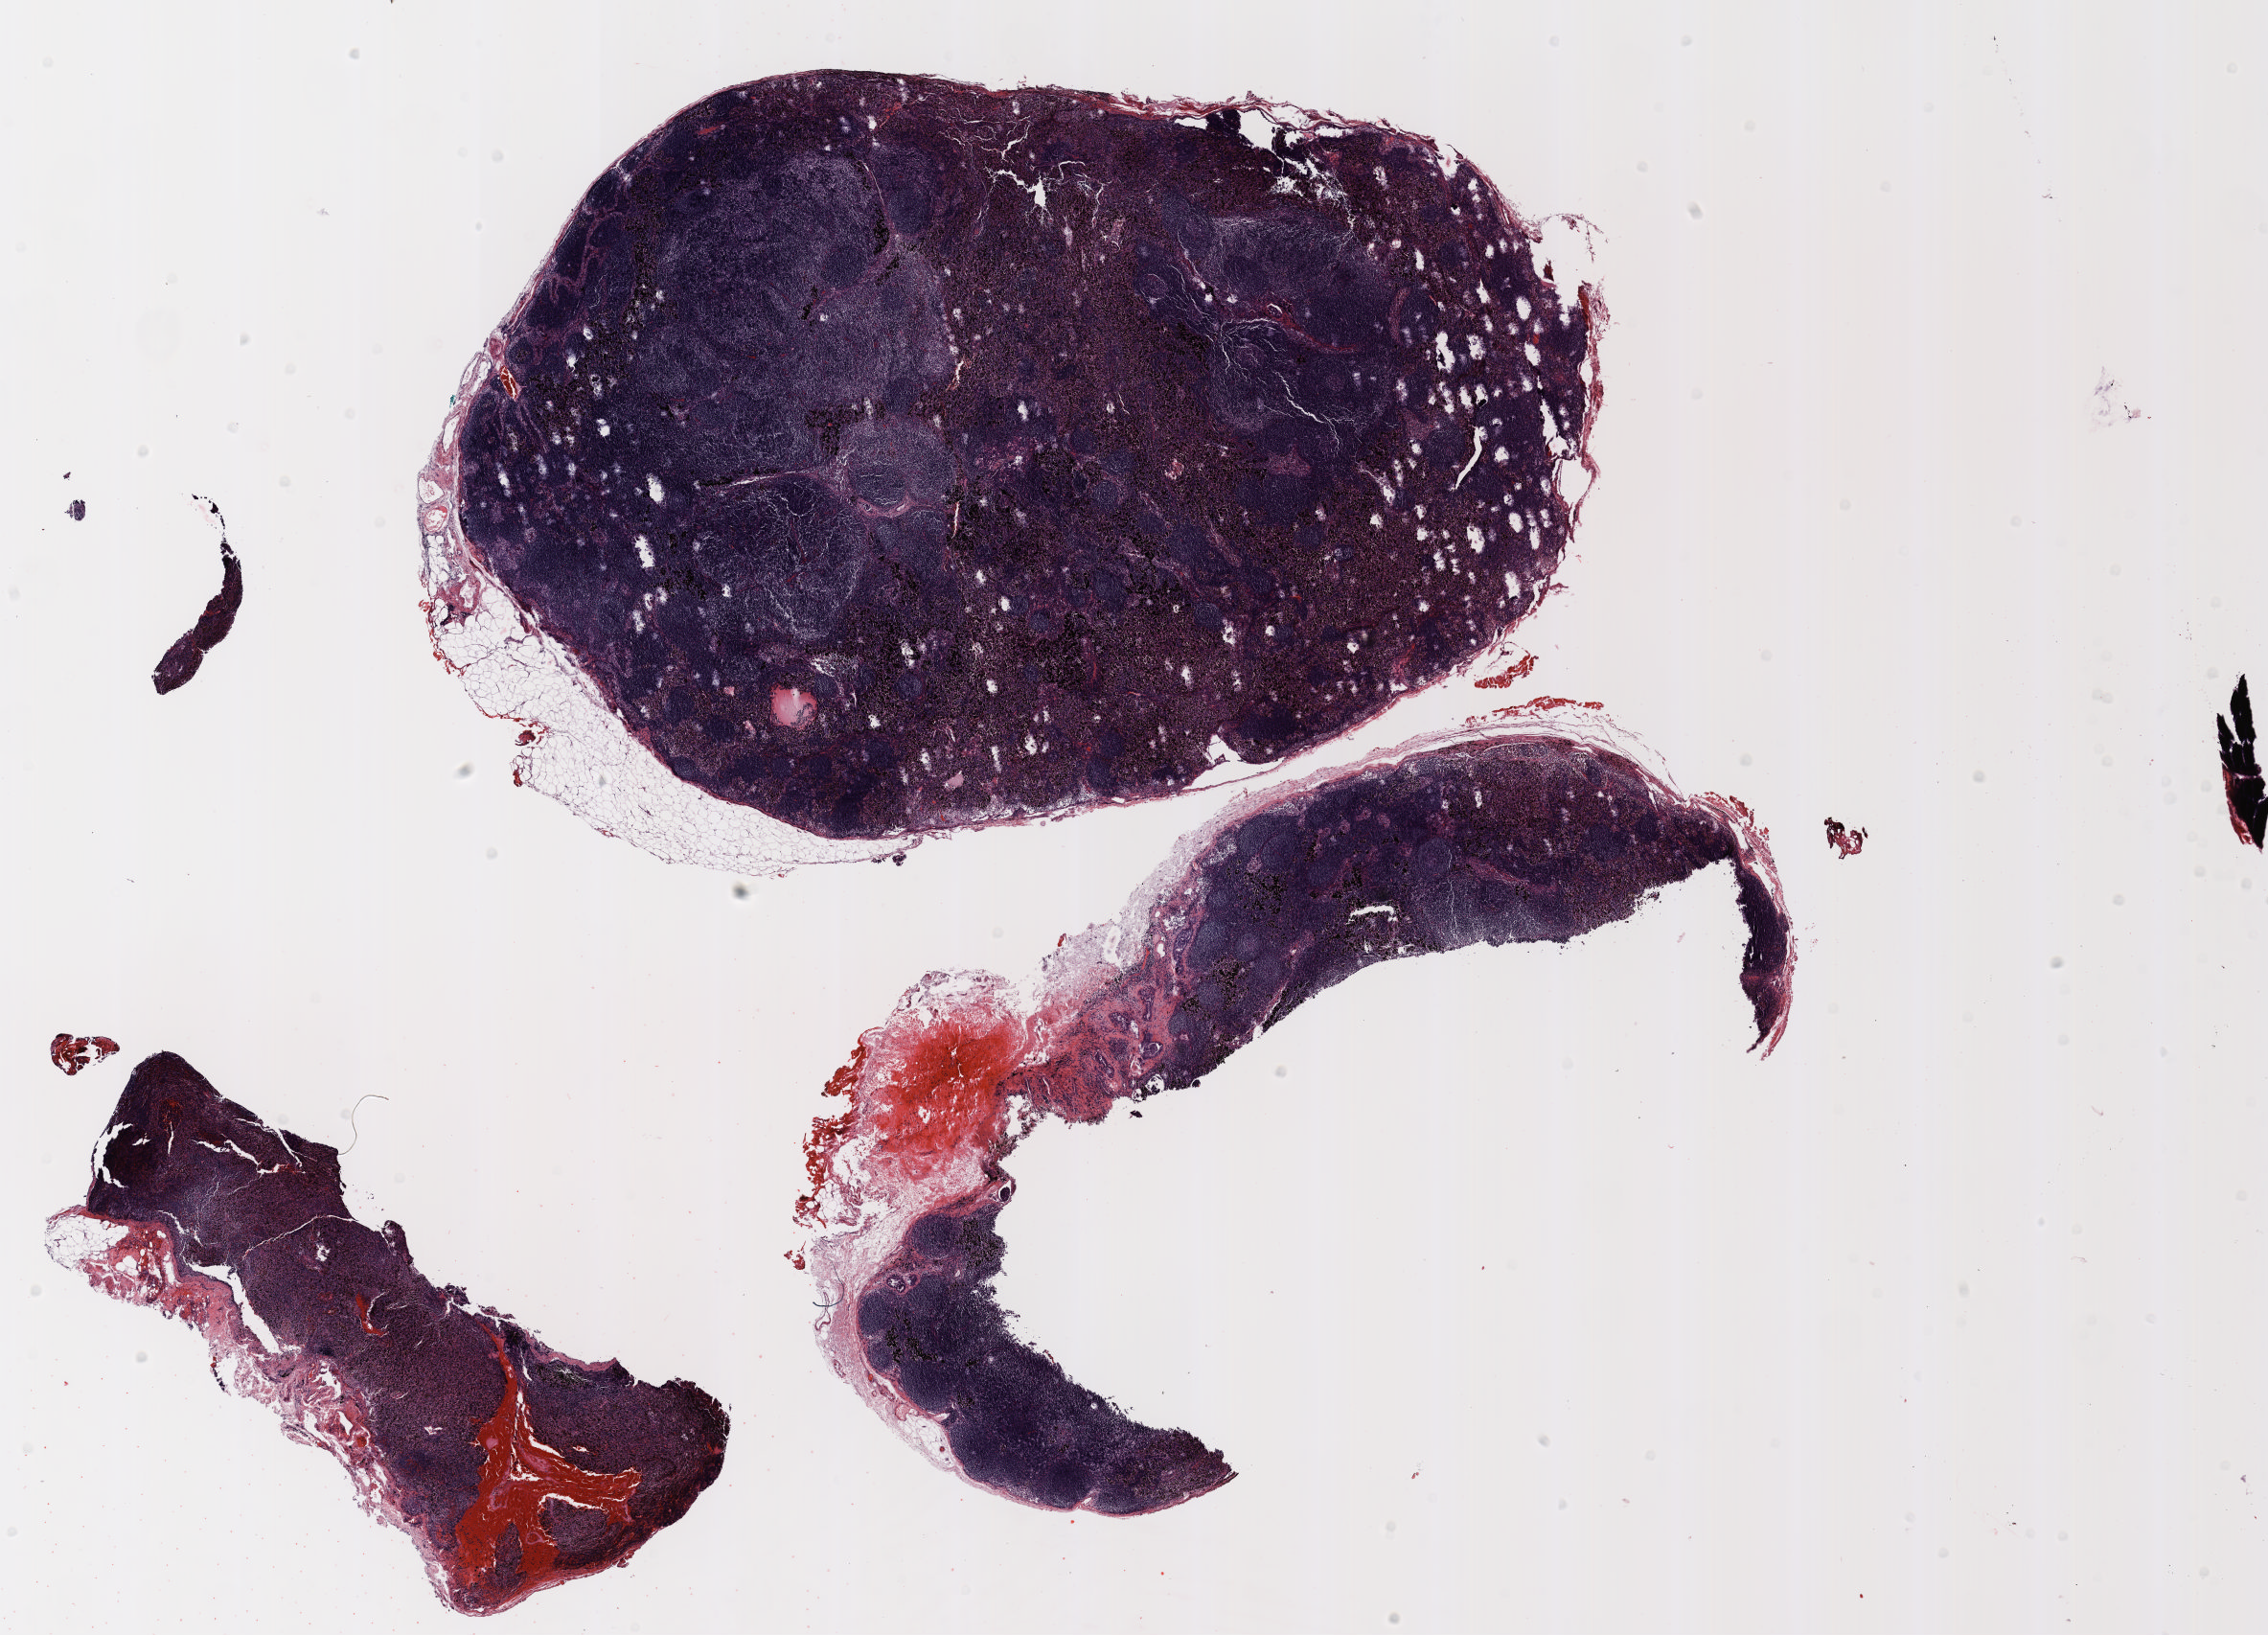
Whole-slide histology image, H&E, whole scanned area (about 19.0 x 13.7 mm, slide scanned at 20x) shown as a low-resolution overview; FFPE section; lung tissue. Male patient, aged 58 at enrolment. Current smoker at enrolment. Grade: poorly differentiated (G3).
Participant's lung-cancer diagnosis: Adenocarcinoma, NOS (ICD-O-3 8140/3). Primary tumour location (clinical record): right lower lobe. Stage (AJCC 6th edition): IIIA. Tumour size (pathology): 15 mm.